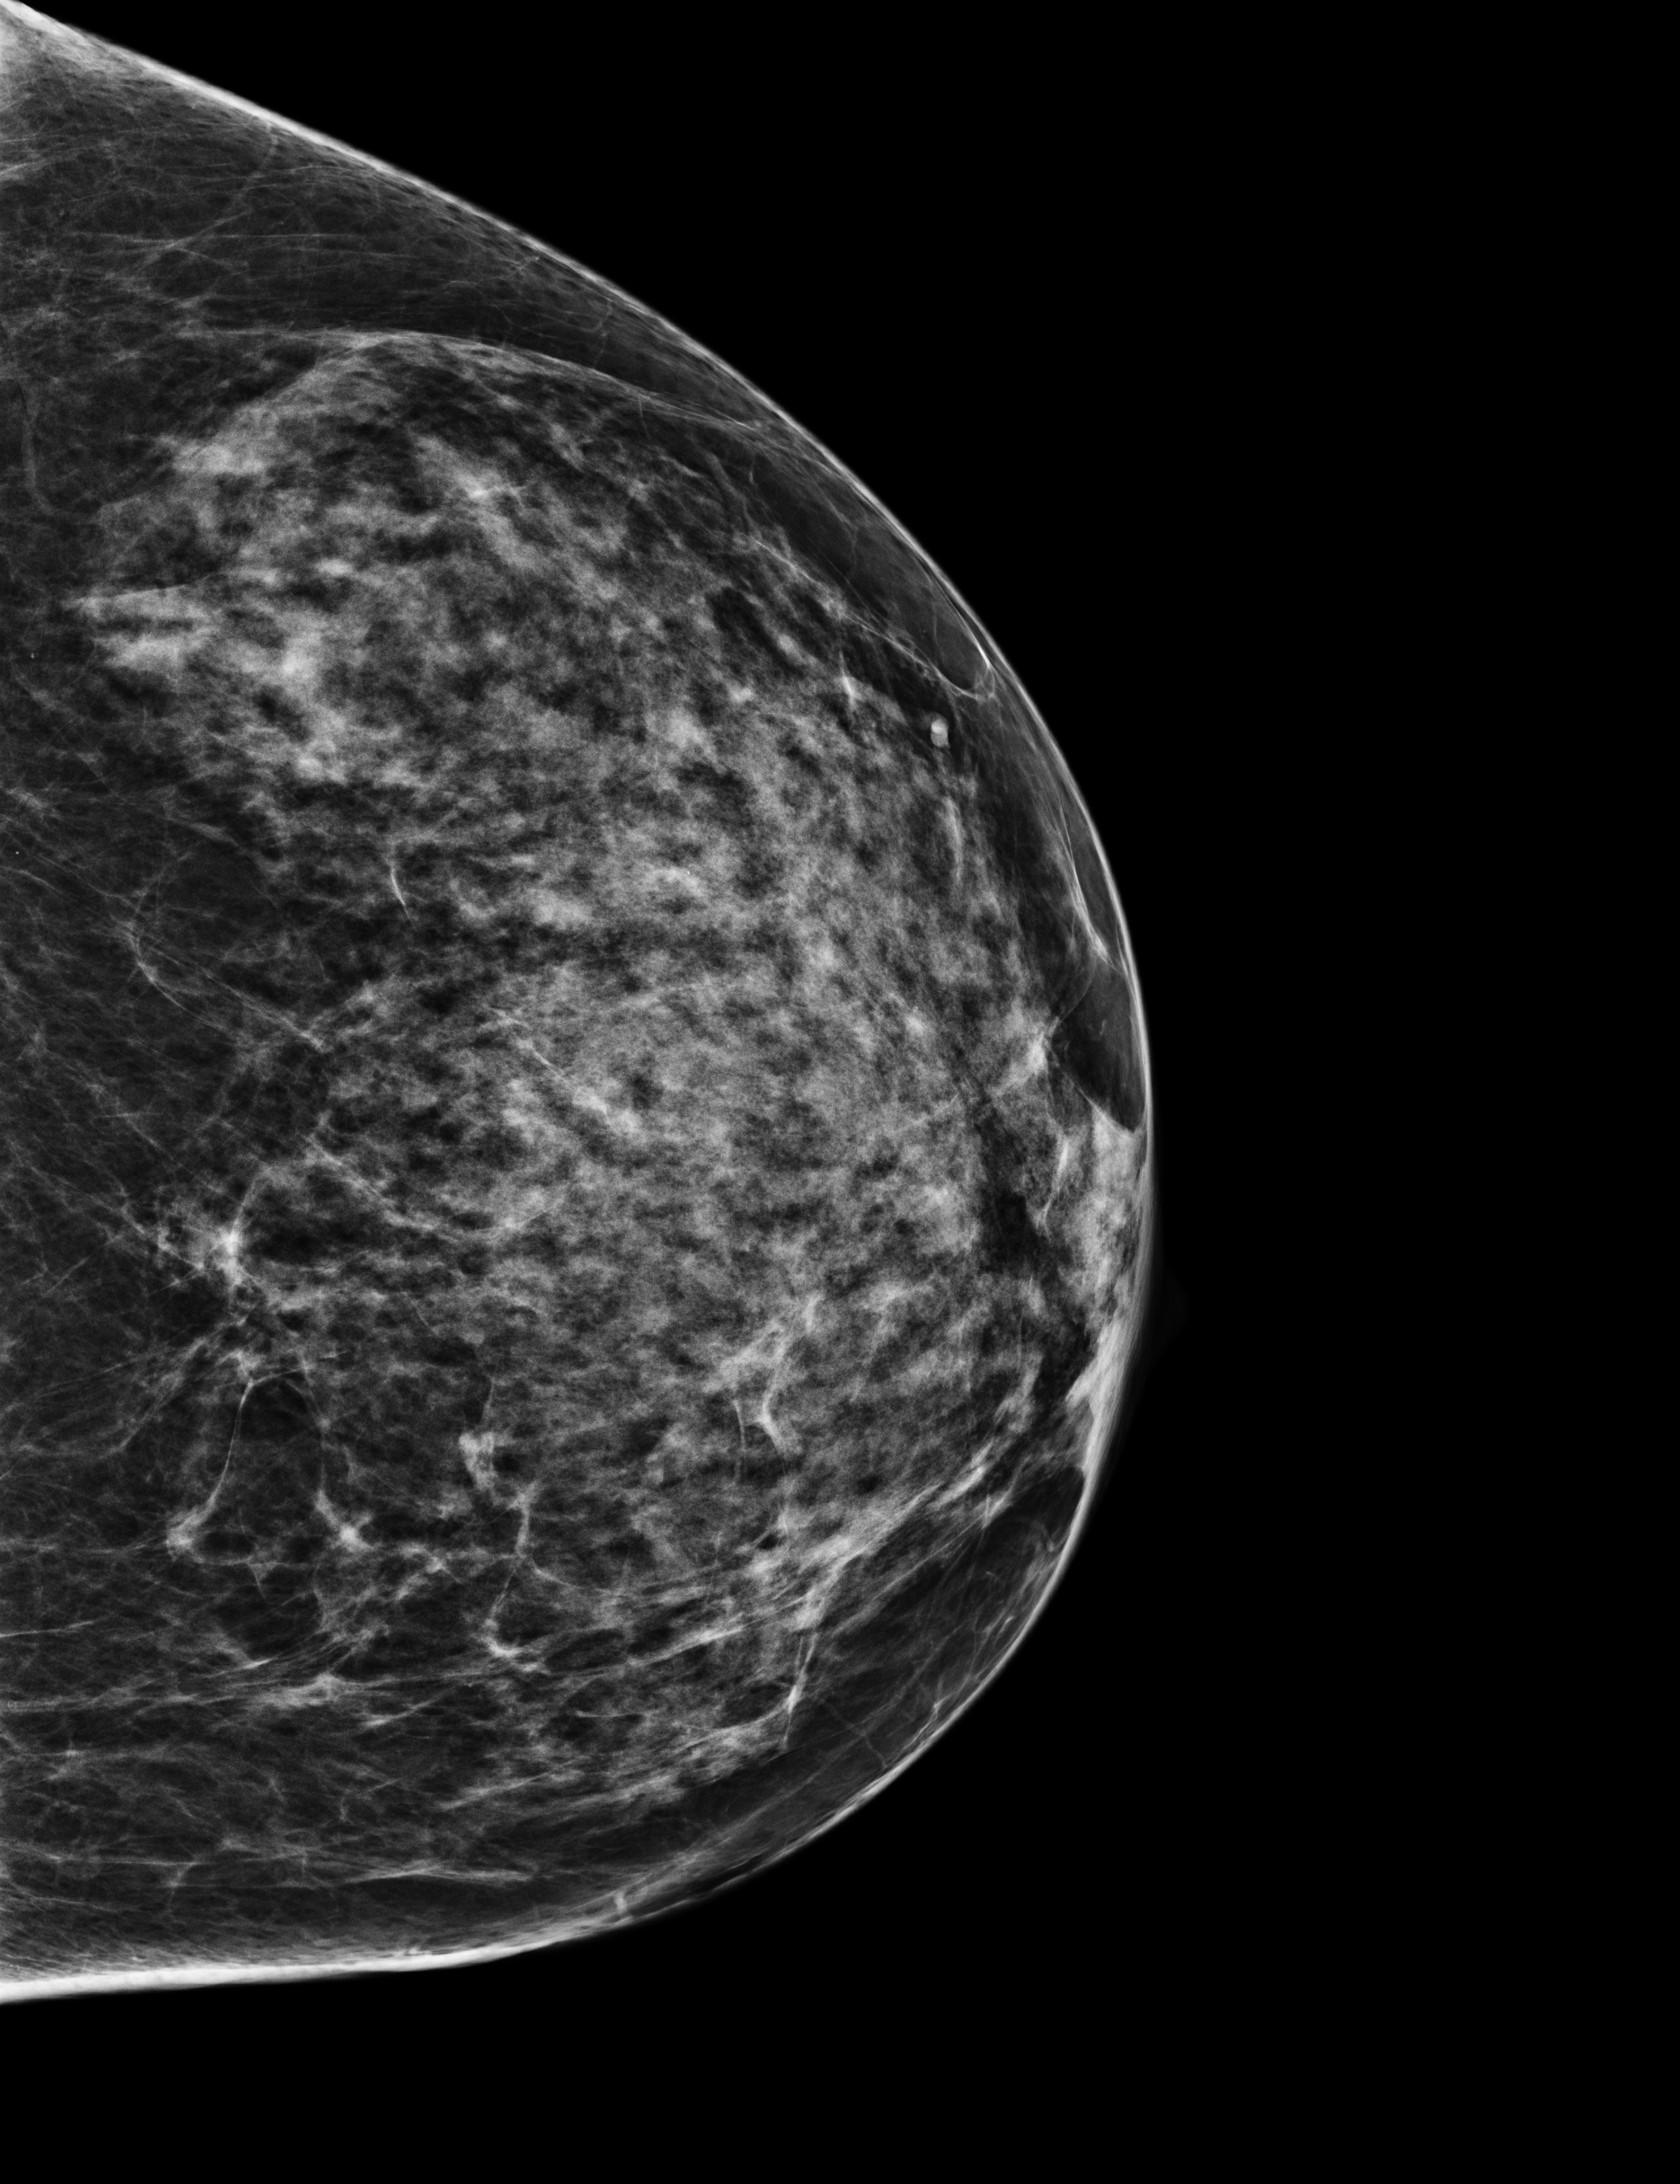
Digital mammogram (FFDM), left breast, CC view, annual screening mammography examination, compressed breast thickness 71 mm. Patient aged 58 years (female).
Breast density at the screening exam (both breasts): heterogeneously dense (BI-RADS density category c). Final BI-RADS category for the screening round (tomosynthesis exam, both breasts): category 1. Recall: no recall after this screen.